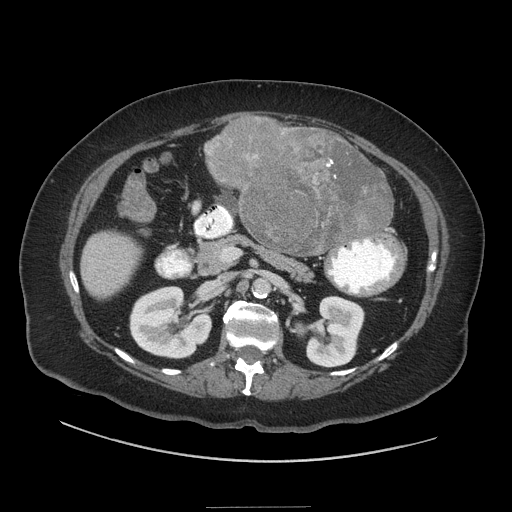
Contrast-enhanced abdominal CT (liver protocol), one axial slice; 140 kVp; soft-tissue window (W 400 / L 40 HU); 2.5 mm slice thickness; 512 × 512 image matrix. Case-level facts recorded for this patient, not image findings: diagnosis: hepatocellular carcinoma (patient treated with transarterial chemoembolisation; whether this scan precedes or follows treatment is not stated here); TNM stage (as recorded): Stage-II; Child-Pugh class: A; tumour nodularity: multinodular; tumour size: 1.7 cm.
Annotated regions visible in this slice (semi-automatic segmentation, software-assisted and operator-edited):
- liver parenchyma outside the tumour (the mass and vessels are separate outlines, so this box may not span the whole liver): box from (x=80, y=132) to (x=394, y=298) px
- mass: (x=206, y=118)–(x=392, y=255)